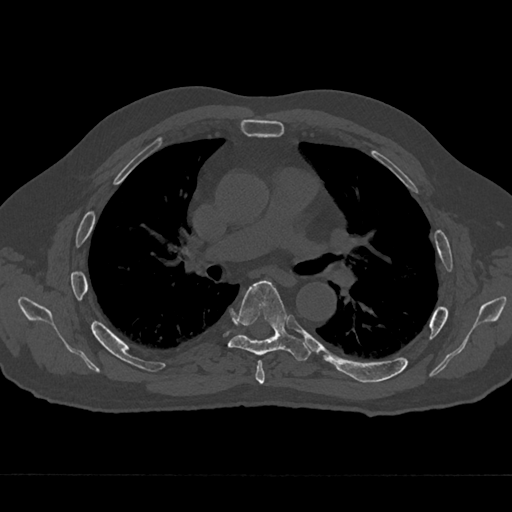
CT including the spine, one axial slice. Slice 427 of 797 in the series (ordered by position). Reconstruction kernel Br40s/3. Bone window (W 1800 / L 400 HU). 0.5 mm slice thickness. 512 × 512 image matrix. Male patient, age 75 years. Case-level facts recorded for this patient, not image findings: primary cancer: renal.
Outlined on this slice (semi-automatic segmentation, software-assisted and operator-edited):
- T5 vertebra: bounding box <255,360,265,385> (left, top, right, bottom; pixels)
- T6 vertebra: <227,280,309,361>